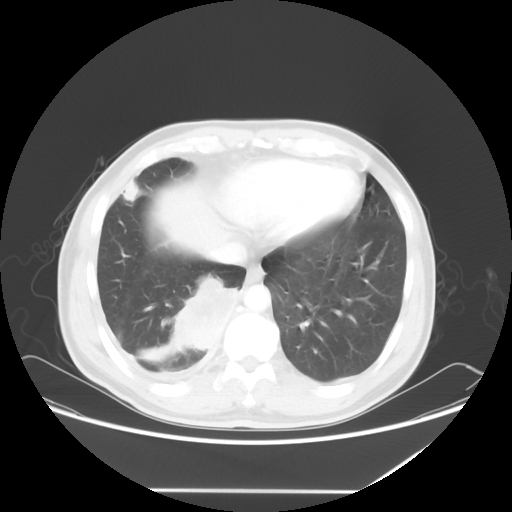
Chest CT, one axial slice; slice 17 of 60 in the series (ordered by position); reconstruction kernel STANDARD; lung window (W 1500 / L -600 HU); 5 mm slice thickness; 512 × 512 image matrix. Male patient, age 48 years. Case-level facts recorded for this patient, not image findings: clinical TNM (as recorded): T3 N3 M1a.
Outlined on this slice (bounding box drawn by a radiologist):
- lung tumour (recorded histology: squamous cell carcinoma): bounding box <162,272,243,351> (left, top, right, bottom; pixels)